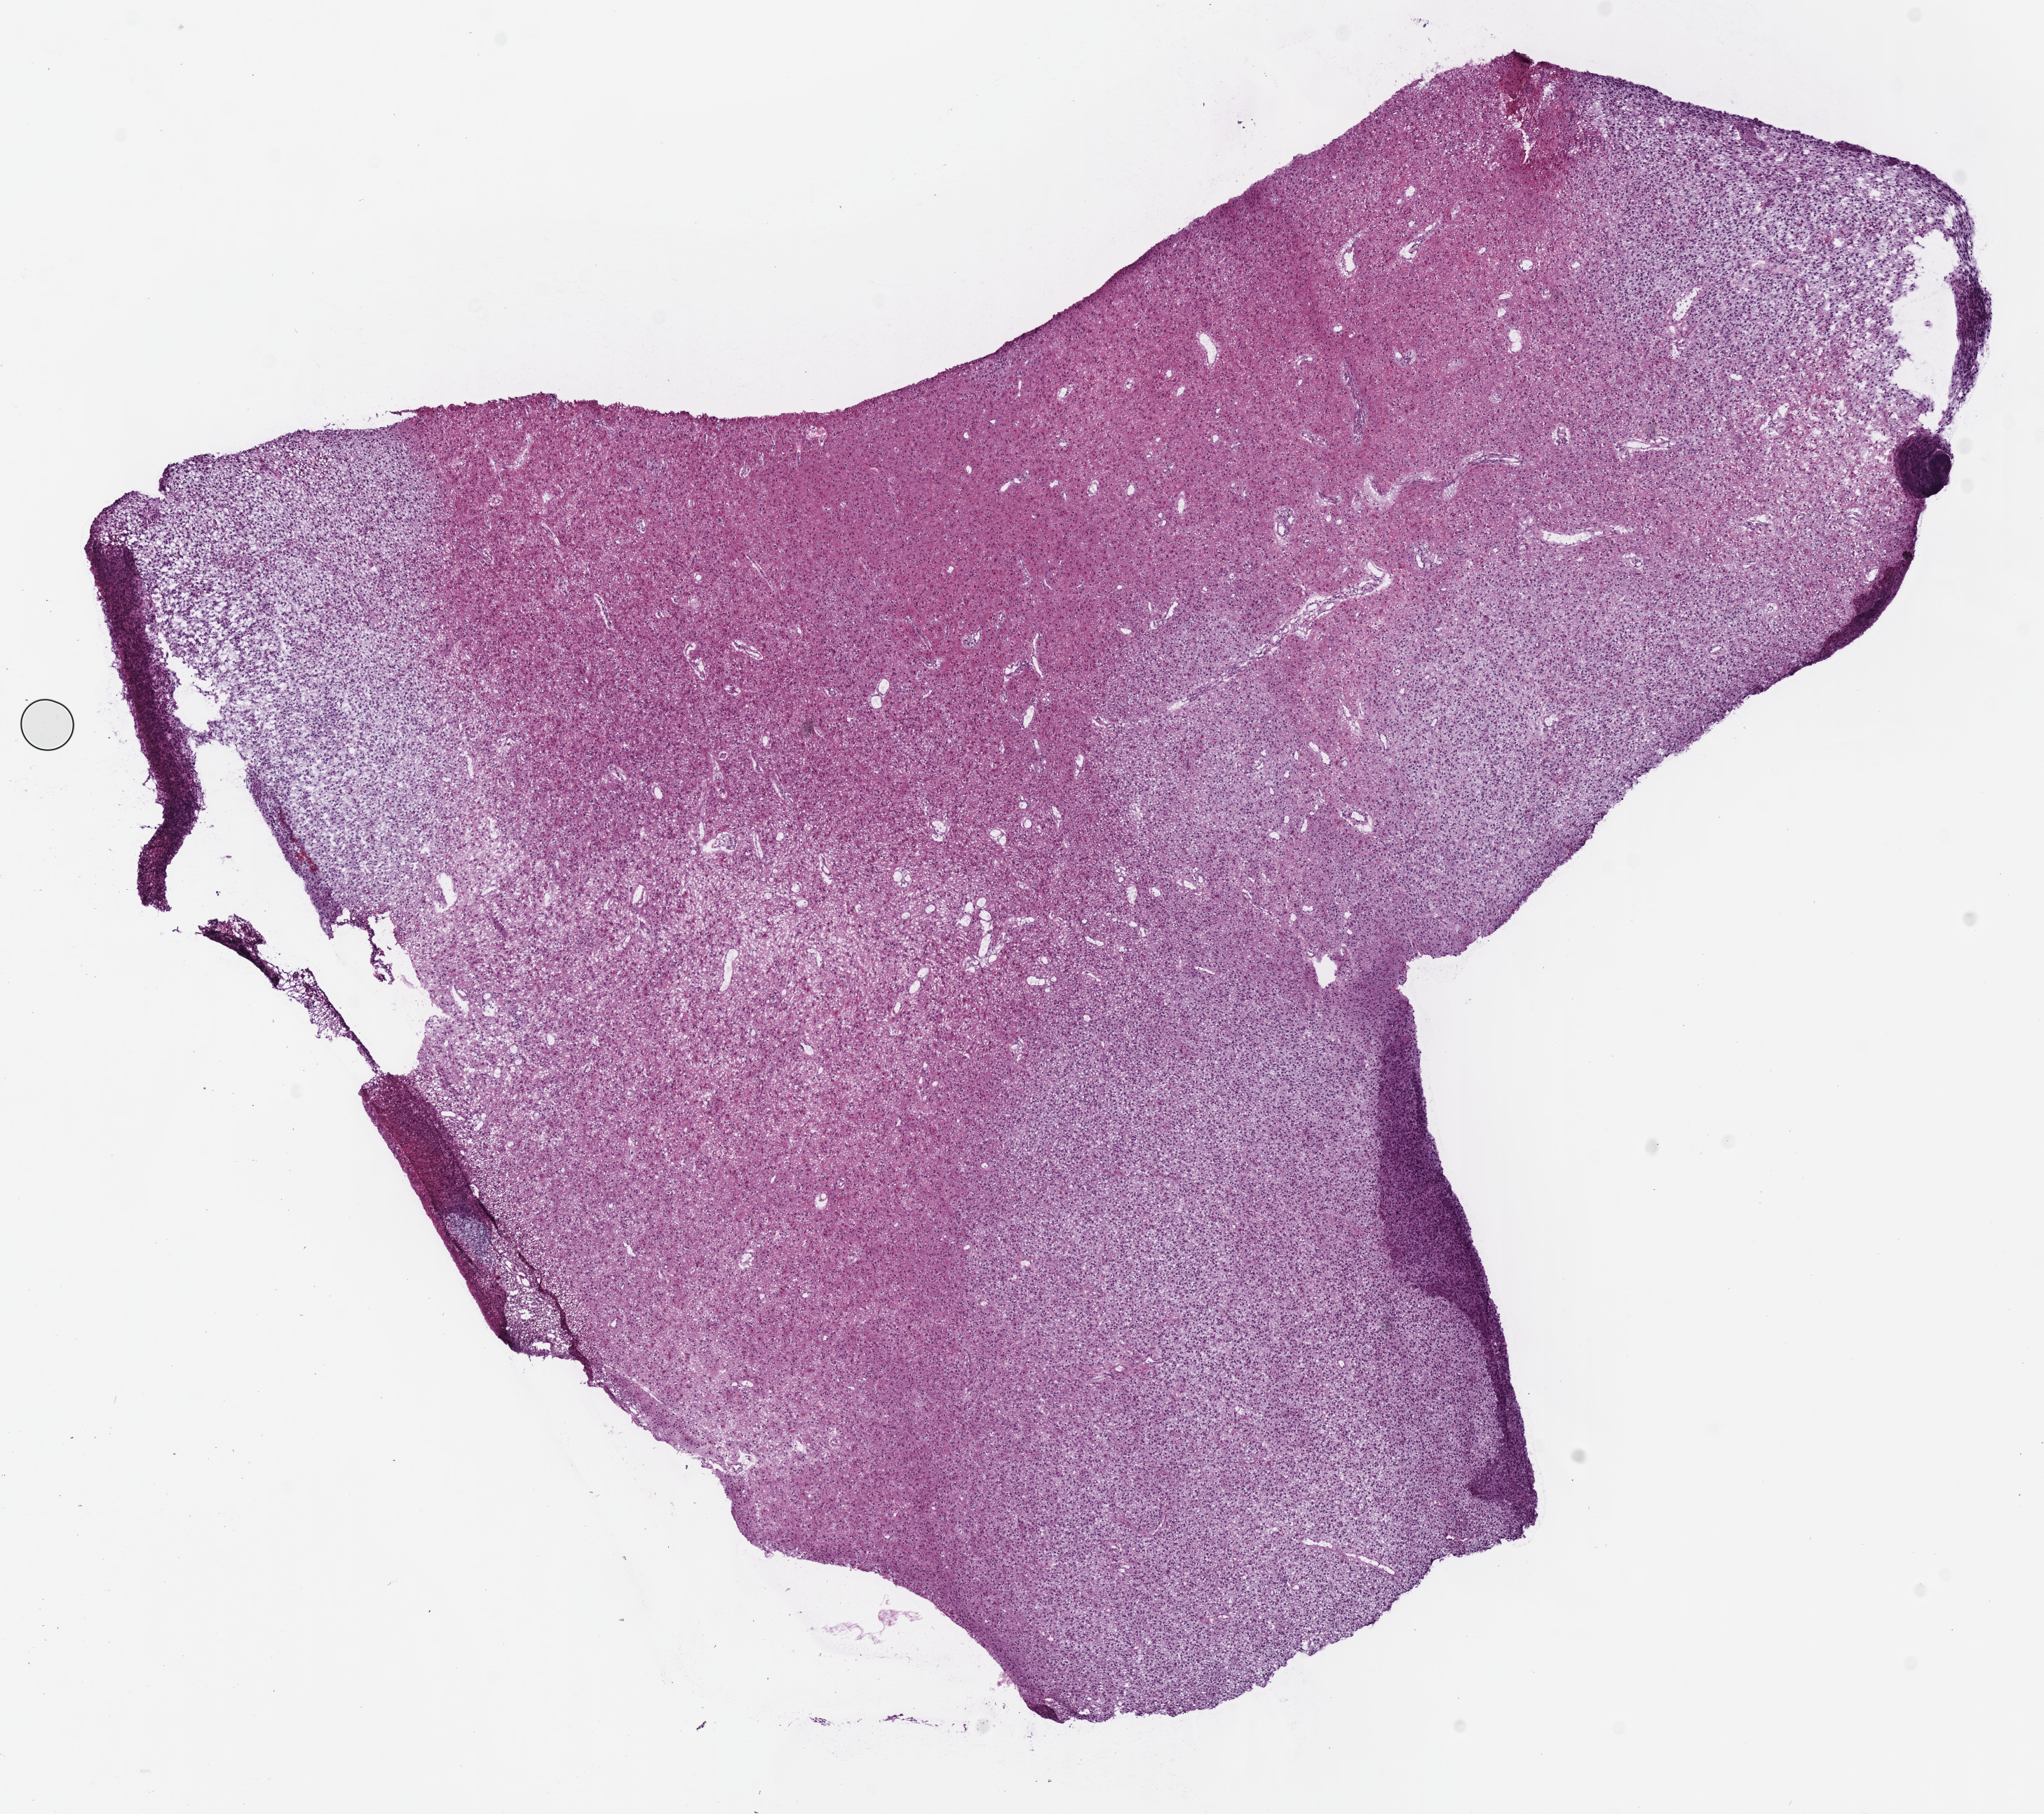
Whole-slide histology image, H&E-stained, shown as a low-resolution overview of the whole scanned area (about 11.5 x 10.2 mm, from a 40x scan); frozen section from the top of the tissue portion; sample: primary tumour, brain. Male patient; age at initial diagnosis 43 years. Histologic grade: G2 (moderately differentiated). Slide review estimates, as recorded: tumour cells 100%, tumour nuclei 85%, normal cells 0%, stromal cells 0%, necrosis 0%.
Laterality: left. Diagnosis: Mixed glioma (cerebrum).